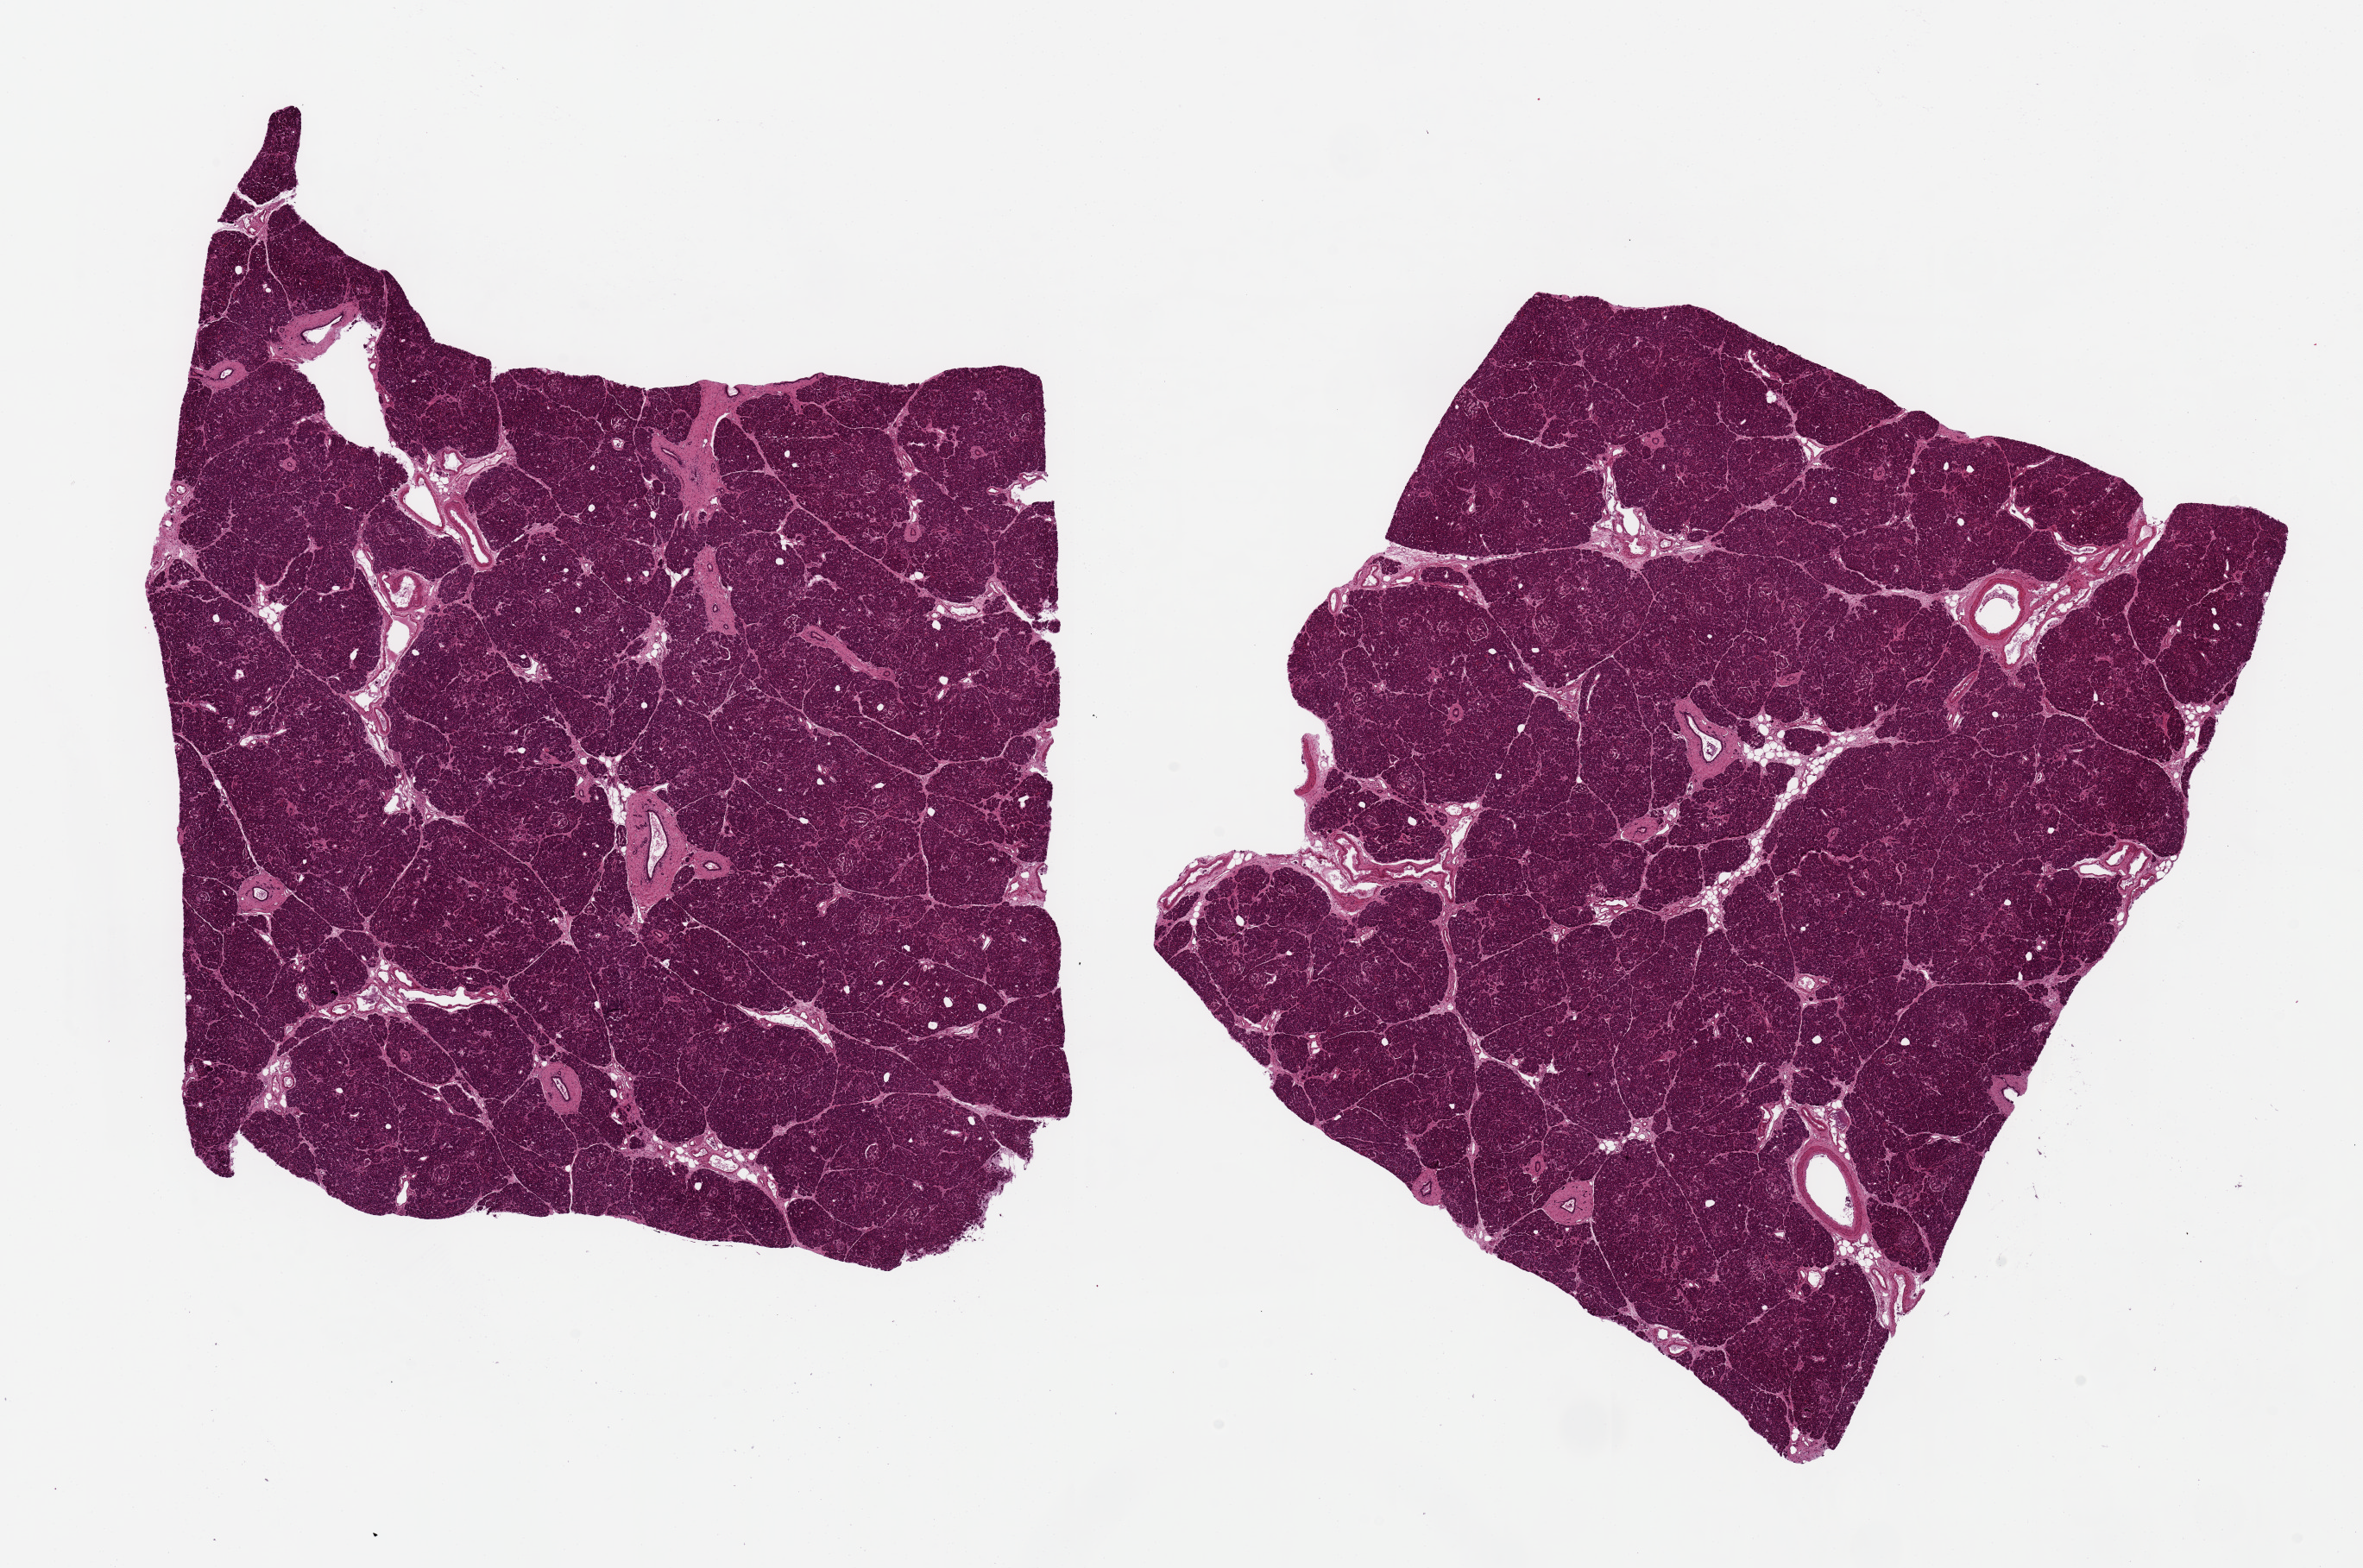
Whole-slide image, hematoxylin and eosin (H&E) stain — a low-resolution overview of the entire scanned area, about 21.7 x 14.4 mm. PAXgene-fixed paraffin-embedded (PFPE) section. Target tissue: pancreas. Tissue donor sample. Donor: female.
Review note (as recorded): 2 ~8.5x8mm aliquots, well preserved, clean with minimal fat.